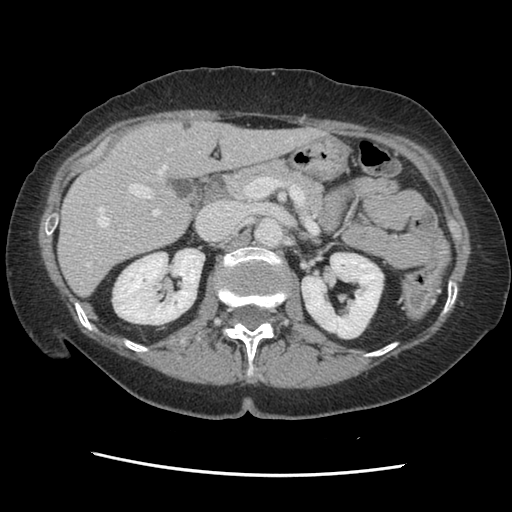
Contrast-enhanced abdominal CT, one axial slice; position 77 of 141 along the scan axis; 120 kVp; soft-tissue window (W 400 / L 40 HU); 2.5 mm slice thickness; 512 × 512 image matrix, field of view 330 × 330 mm. Female patient, age 61 years. Case-level facts recorded for this patient, not image findings: diagnosis: colorectal cancer liver metastases, imaged before liver resection; multiple liver metastases: no; largest metastasis: 2.4 cm; disease in both lobes: no.
Outlined on this slice (expert manual segmentation):
- hepatic veins: box from (x=86, y=138) to (x=292, y=266) px
- liver: (x=59, y=122)–(x=314, y=295)
- planned liver remnant (the part of the liver to remain after resection): (x=59, y=122)–(x=314, y=295)
- portal vein (with intrahepatic branches): (x=90, y=184)–(x=160, y=247)
- liver metastasis: (x=183, y=121)–(x=193, y=132)